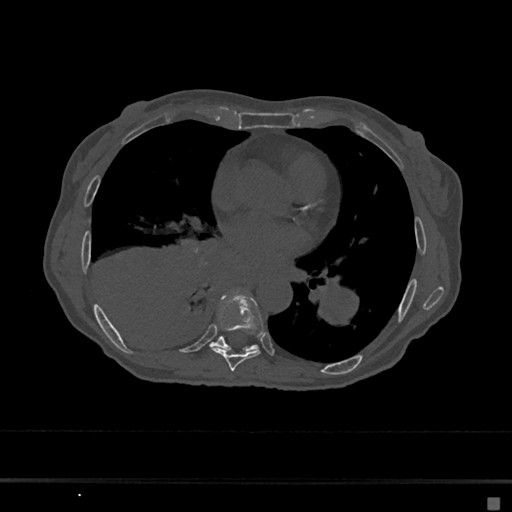
CT including the spine, one axial slice; position 354 of 797 along the scan axis; reconstruction kernel Br40s/3; bone window (W 1800 / L 400 HU); 512 × 512 image matrix, field of view 360 × 360 mm. Female patient, age 68 years. From the clinical record (not read from this slice): primary cancer: renal.
Annotated regions visible in this slice (semi-automatically segmented with operator editing):
- T7 vertebra: bounding box [x1, y1, x2, y2] px = [212, 294, 264, 371]
- T8 vertebra: [211, 337, 258, 352]